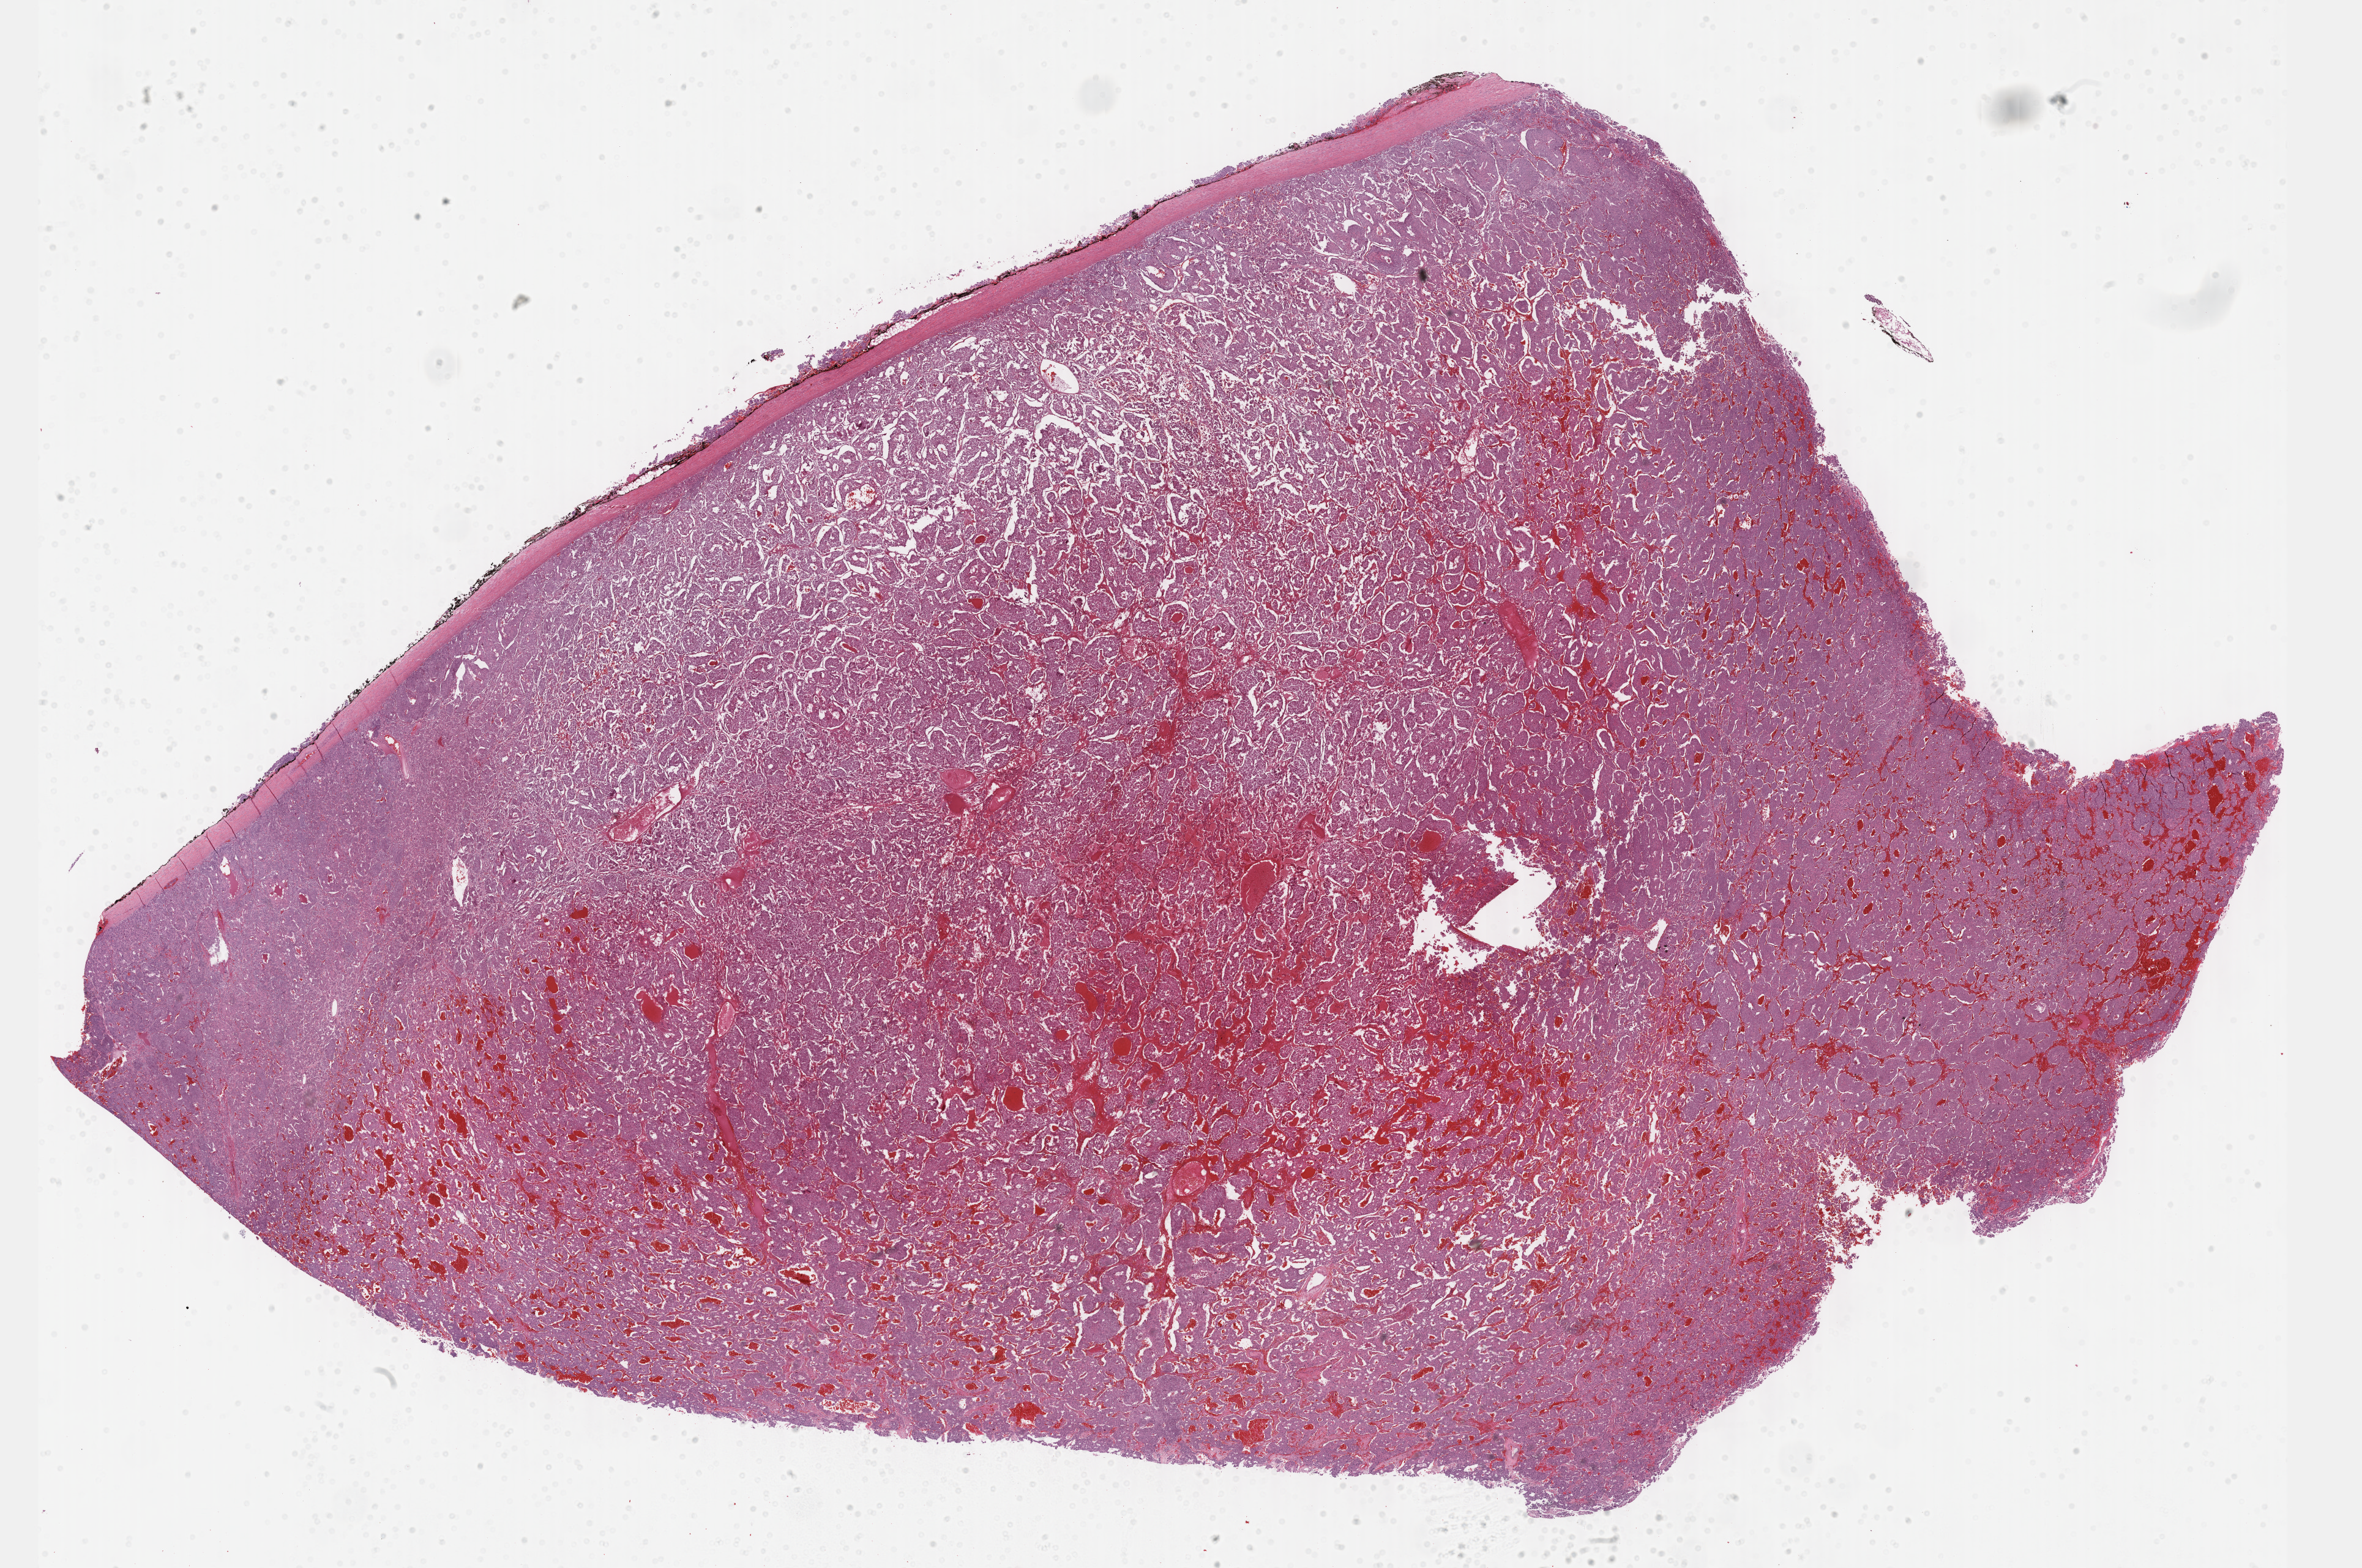
Digitized H&E-stained tissue section (whole slide) — whole scanned area (about 31.2 x 20.7 mm, acquisition: 40x scan) shown as a low-resolution overview. FFPE section. Sample: primary tumour, adrenal gland. Female, age 30 years at initial diagnosis.
- histologic diagnosis: Pheochromocytoma, NOS